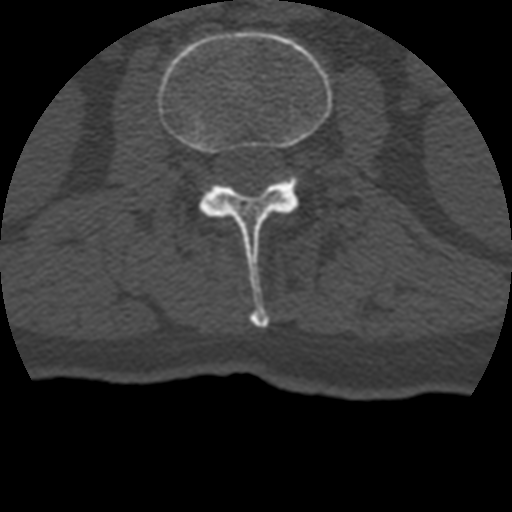
CT including the spine, one axial slice. Slice 113 of 399 in the series (ordered by position). 120 kVp. Bone window (W 1800 / L 400 HU). 512 × 512 image matrix, field of view 160 × 160 mm. Patient age 69 years. Case-level facts recorded for this patient, not image findings: primary cancer: prostate.
Annotated regions visible in this slice (semi-automatic segmentation, software-assisted and operator-edited):
- L2 vertebra: bounding box (x1, y1, x2, y2) in pixels: (158, 31, 332, 328)